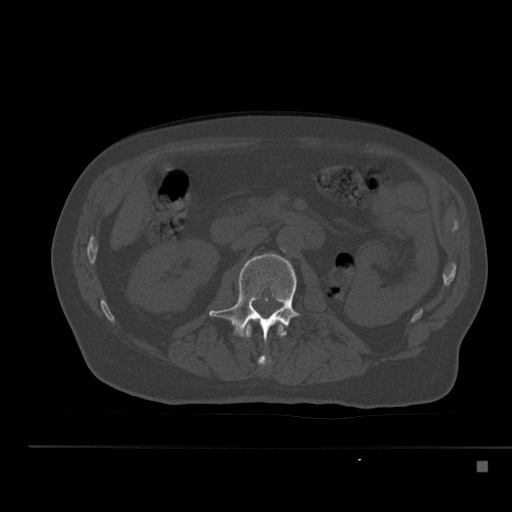
CT including the spine, one axial slice; slice 187 of 517 in the series (ordered by position); reconstruction kernel Br40s; 120 kVp; bone window (W 1800 / L 400 HU); 1.5 mm slice thickness; 512 × 512 image matrix. Patient: male, 70 years. Case-level facts recorded for this patient, not image findings: primary cancer: renal.
Annotated regions visible in this slice (semi-automatic segmentation, software-assisted and operator-edited):
- L1 vertebra: bounding box <244,320,286,367> (left, top, right, bottom; pixels)
- L2 vertebra: <209,253,300,341>